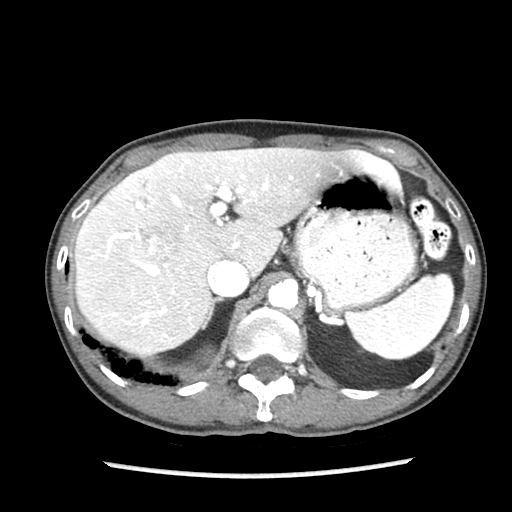
Contrast-enhanced abdominal CT (liver protocol), one axial slice. Slice 60 of 87 in the series (ordered by position). 140 kVp. Soft-tissue window (W 400 / L 40 HU). 2.5 mm slice thickness. 512 × 512 image matrix, field of view 300 × 300 mm. Case-level facts recorded for this patient, not image findings: diagnosis: hepatocellular carcinoma (patient treated with transarterial chemoembolisation; whether this scan precedes or follows treatment is not stated here); TNM stage (as recorded): Stage-IIIB; Child-Pugh class: A; tumour differentiation: well differentiated; tumour nodularity: uninodular.
Outlined on this slice (semi-automatically segmented with operator editing):
- liver parenchyma outside the tumour (the mass and vessels are separate outlines, so this box may not span the whole liver): bounding box (x1, y1, x2, y2) in pixels: (74, 148, 388, 356)
- mass: (146, 233, 176, 261)
- liver vessels: (105, 155, 388, 325)